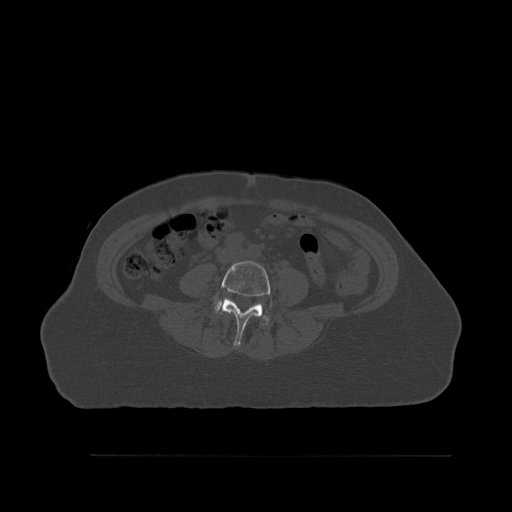
CT including the spine, one axial slice; slice 205 of 527 in the series (ordered by position); bone window (W 1800 / L 400 HU); 1.5 mm slice thickness; 512 × 512 image matrix. Patient: female, 73 years. Case-level facts recorded for this patient, not image findings: primary cancer: breast; vertebrae with lytic lesions (as recorded): L2.
Structures marked on this image (semi-automatic segmentation, software-assisted and operator-edited):
- L4 vertebra: bounding box [x1, y1, x2, y2] px = [212, 261, 273, 346]
- L5 vertebra: [214, 301, 269, 325]